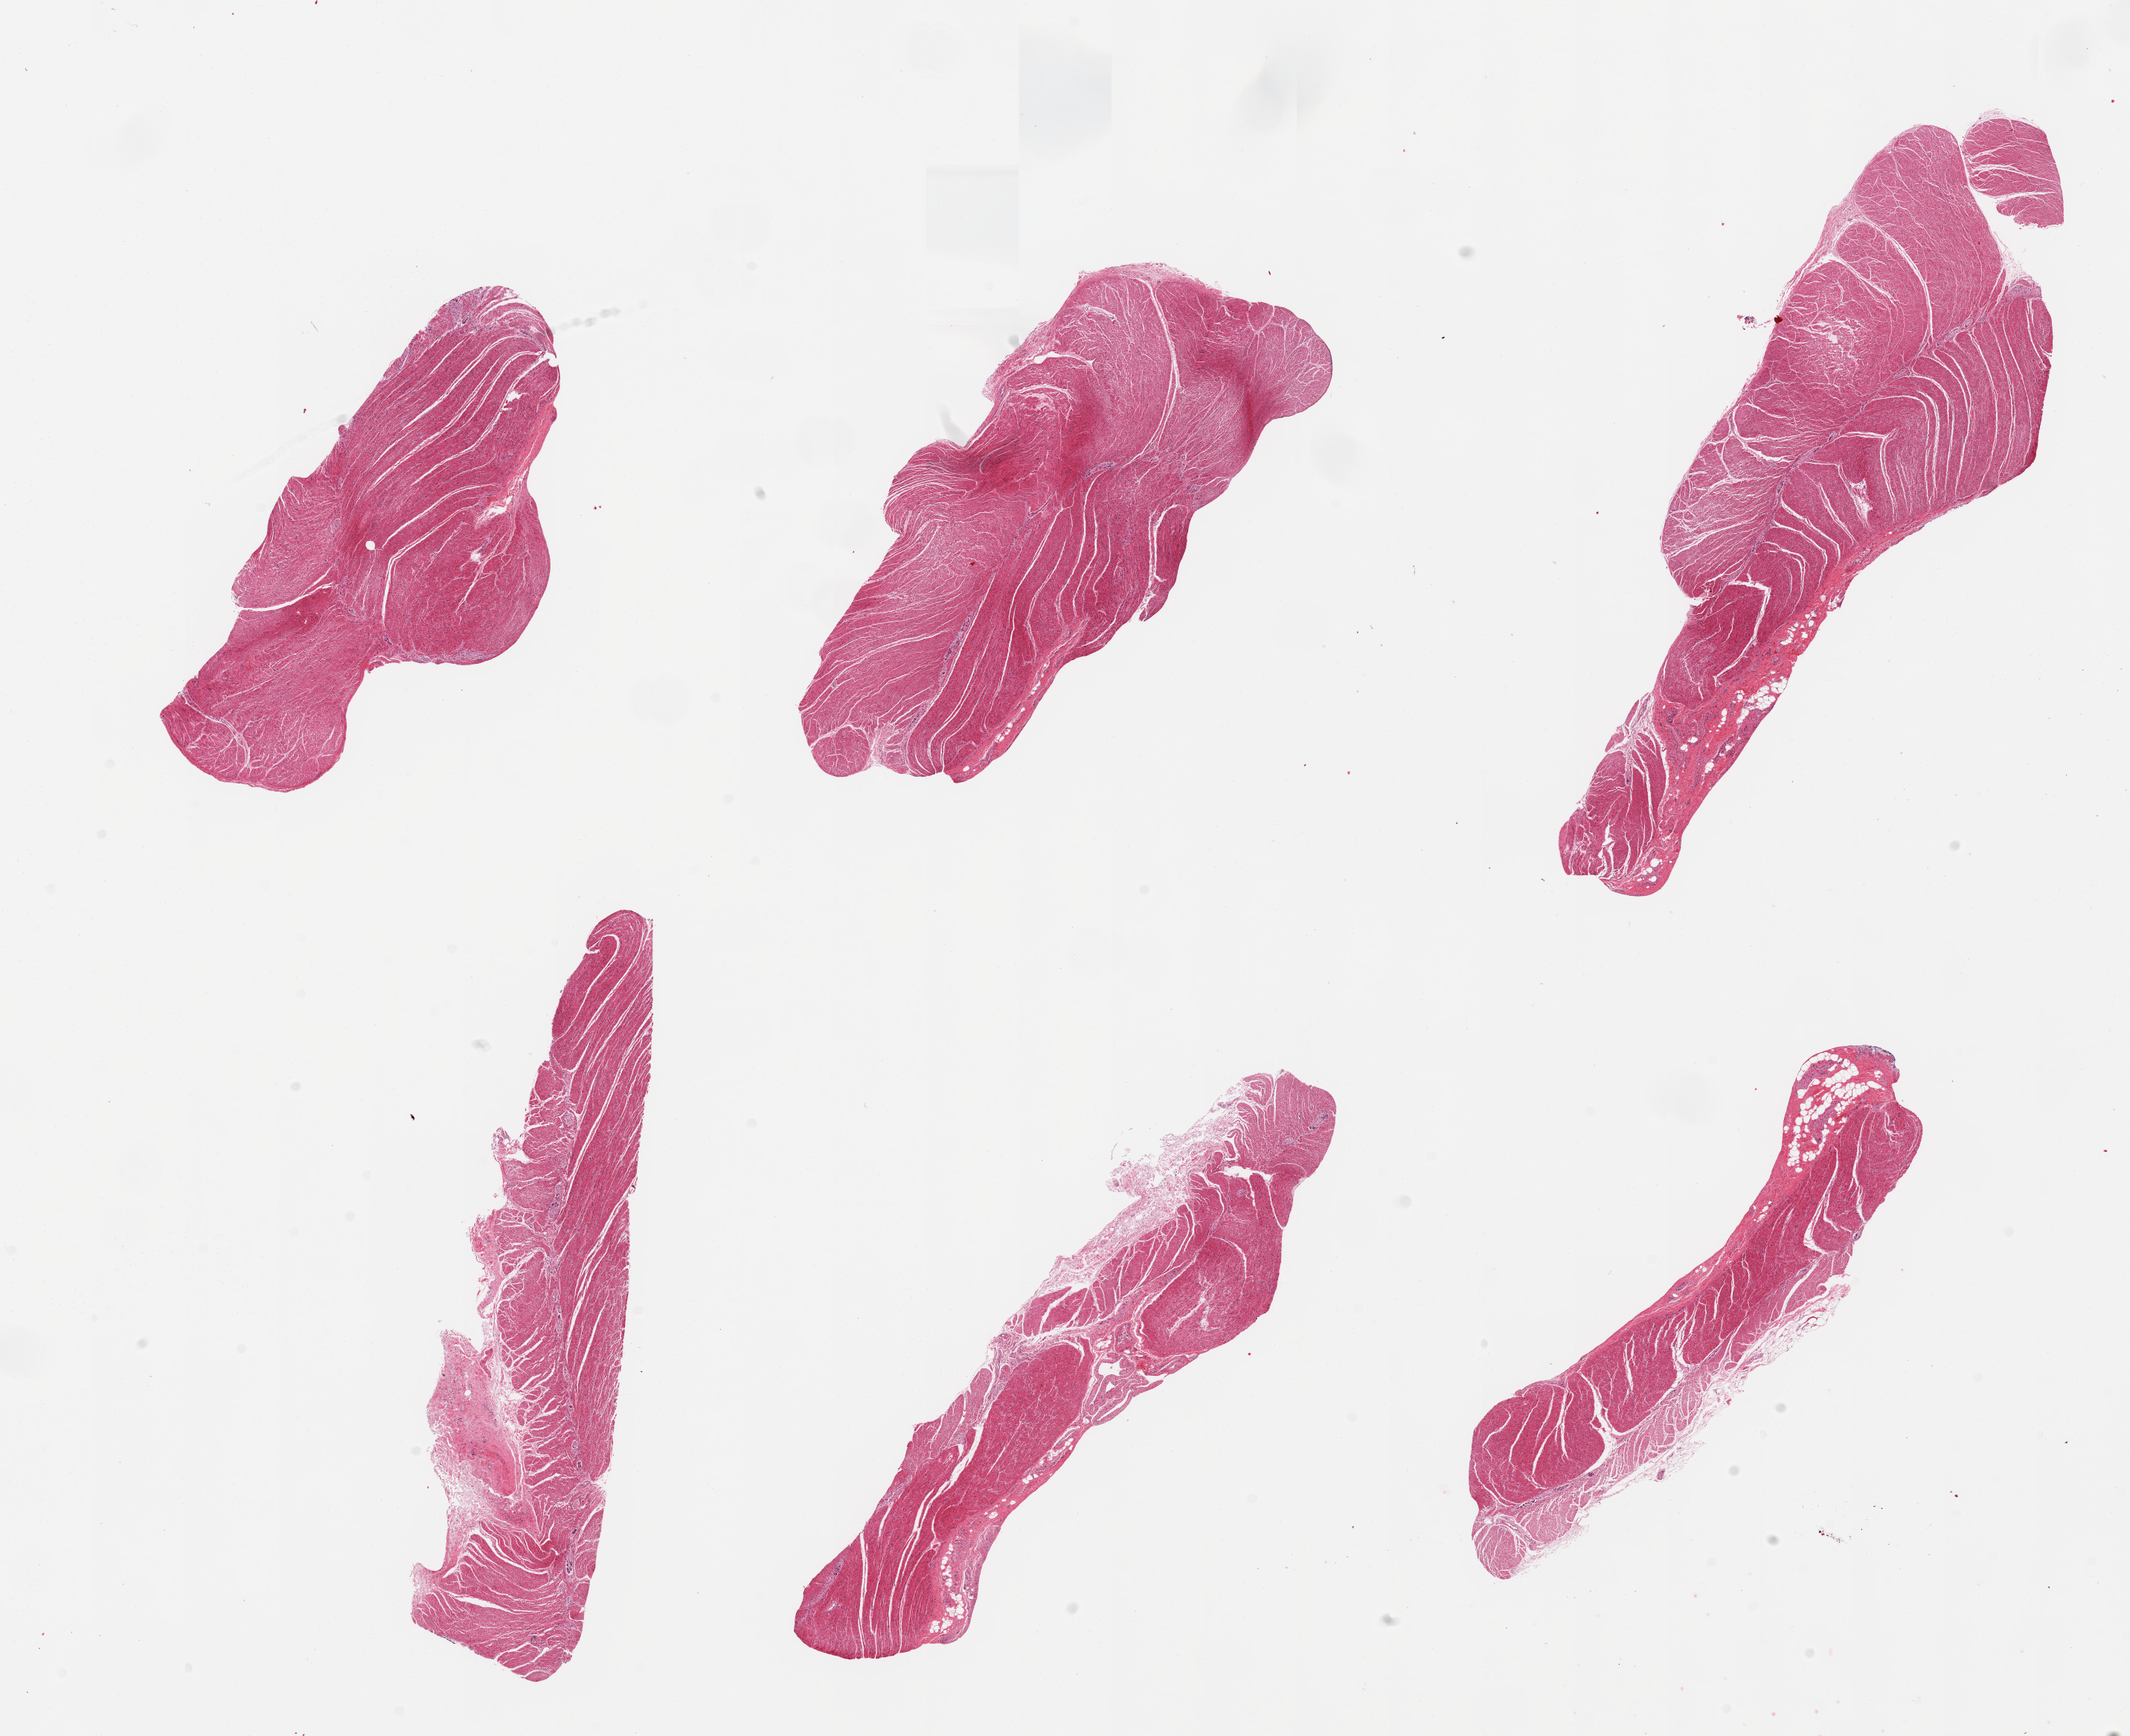
H&E whole-slide image, brightfield, a low-resolution overview of the entire scanned area, about 22.6 x 18.5 mm. PAXgene-fixed, paraffin-embedded tissue. Target tissue: sigmoid colon. Donor tissue sample.
Reviewer comment on this tissue sample: 6 pieces, all muscularis, good specimens.